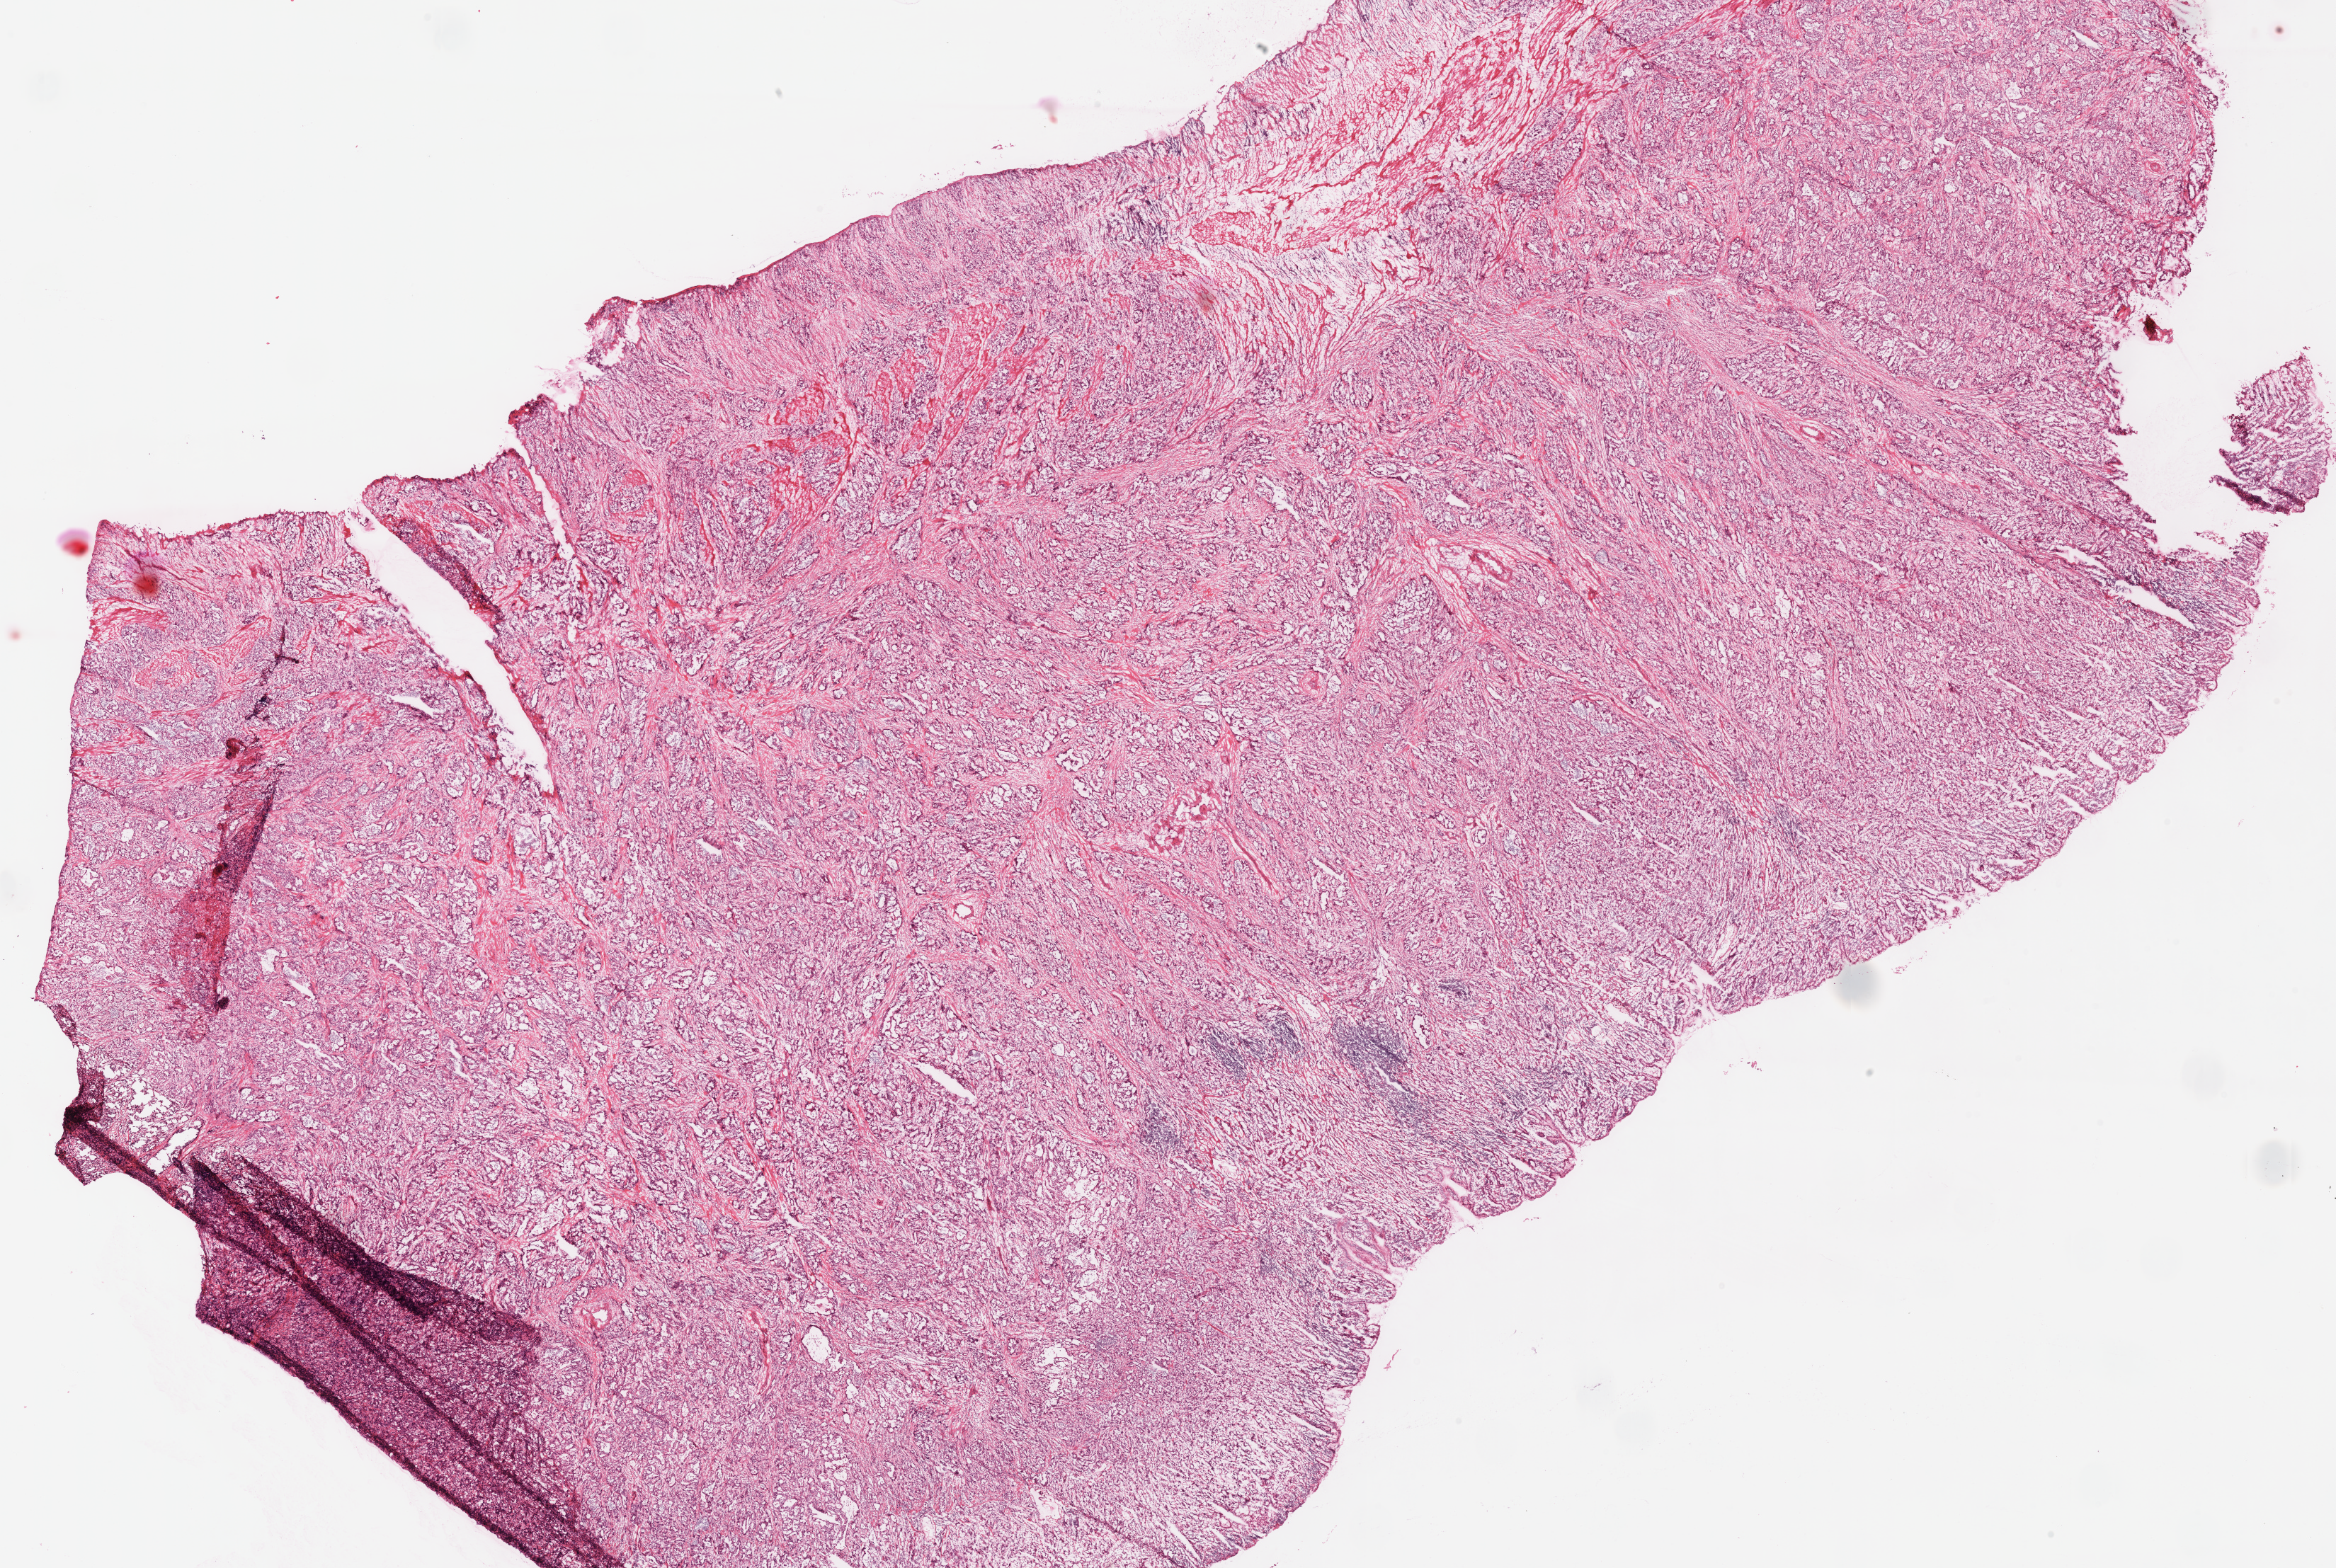
Digitized Hematoxylin and eosin (H&E) stained tissue section (whole slide) — low-resolution overview of the scanned area, about 25.9 x 17.4 mm (from a 40x scan), frozen section, primary tumour sample from the stomach. Patient: female, age at initial diagnosis 58 years. Histologic grade: G3 (poorly differentiated). Slide review estimates, as recorded: tumour cells 80%, tumour nuclei 80%, normal cells 0%, stromal cells 15%, necrosis 5%.
Pathologic diagnosis: Adenocarcinoma, intestinal type (body of stomach). TNM: T4b N2 M0. AJCC pathologic stage: IIIC (7th edition).